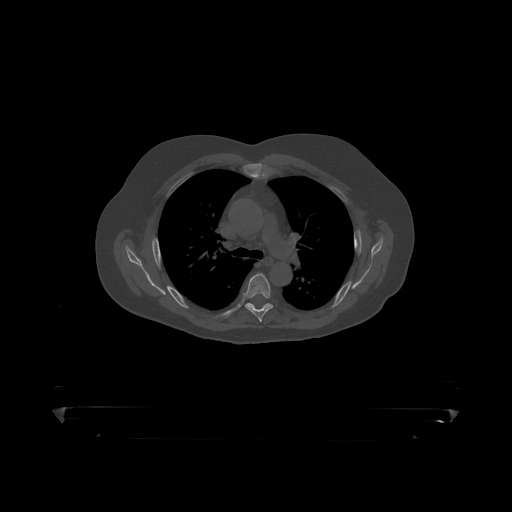
CT including the spine, one axial slice; slice 317 of 390 in the series (ordered by position); reconstruction kernel STANDARD; 120 kVp; bone window (W 1800 / L 400 HU); 512 × 512 image matrix, field of view 650 × 650 mm. Patient: male, 60 years. From the clinical record (not read from this slice): primary cancer: prostate.
Annotated regions visible in this slice (semi-automatically segmented with operator editing):
- T5 vertebra: bounding box [x1, y1, x2, y2] px = [244, 274, 273, 319]
- T6 vertebra: [246, 303, 273, 308]